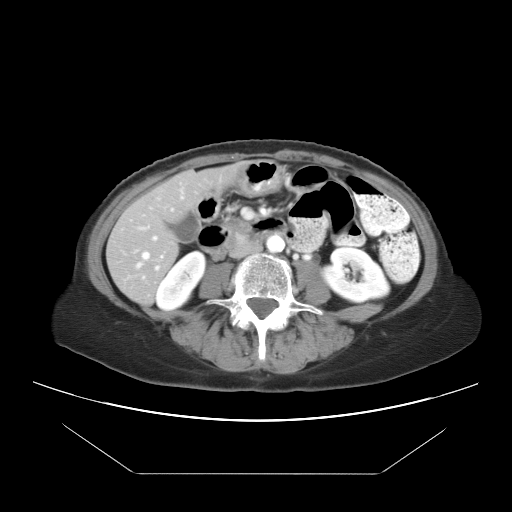
Contrast-enhanced abdominal CT, one axial slice; position 5 of 21 along the scan axis; reconstruction kernel STANDARD; 120 kVp; intravenous contrast given; soft-tissue window (W 400 / L 40 HU); 512 × 512 image matrix. Female patient, age 72 years. Case-level facts recorded for this patient, not image findings: diagnosis: colorectal cancer liver metastases, imaged before liver resection; multiple liver metastases: yes; largest metastasis: 4 cm.
Annotated regions visible in this slice (manually delineated by an expert):
- hepatic veins: box from (x=135, y=209) to (x=173, y=269) px
- liver: (x=108, y=168)–(x=228, y=304)
- planned liver remnant (the part of the liver to remain after resection): (x=108, y=169)–(x=228, y=294)
- portal vein (with intrahepatic branches): (x=139, y=226)–(x=164, y=259)